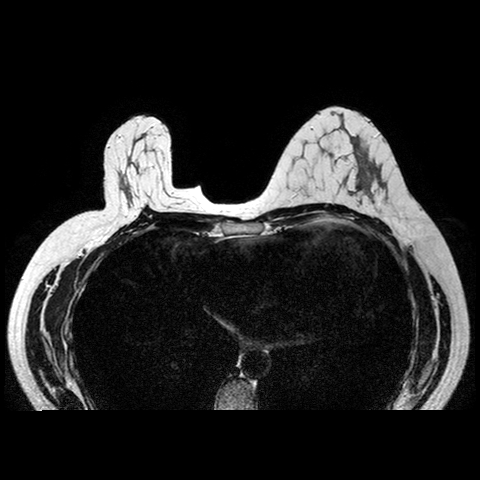
Breast MRI examination; 2 images, each one mid-volume slice chosen by position. Patient in her 40s.
Image 1: axial T2-weighted / STIR image, slice 13 of 24, 3 mm slice thickness.
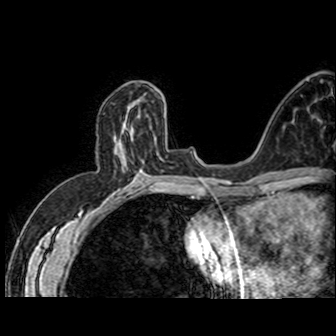
Image 2: axial dynamic contrast-enhanced T1-weighted image, series "AX BLISS", slice 26 of 50, 4 mm slice thickness.
Patient-level pathology facts (from the clinical record, not from the images): pathology diagnosis: ductal CA in situ (left breast); pathology report notes: Ductal carcinoma in-situ.